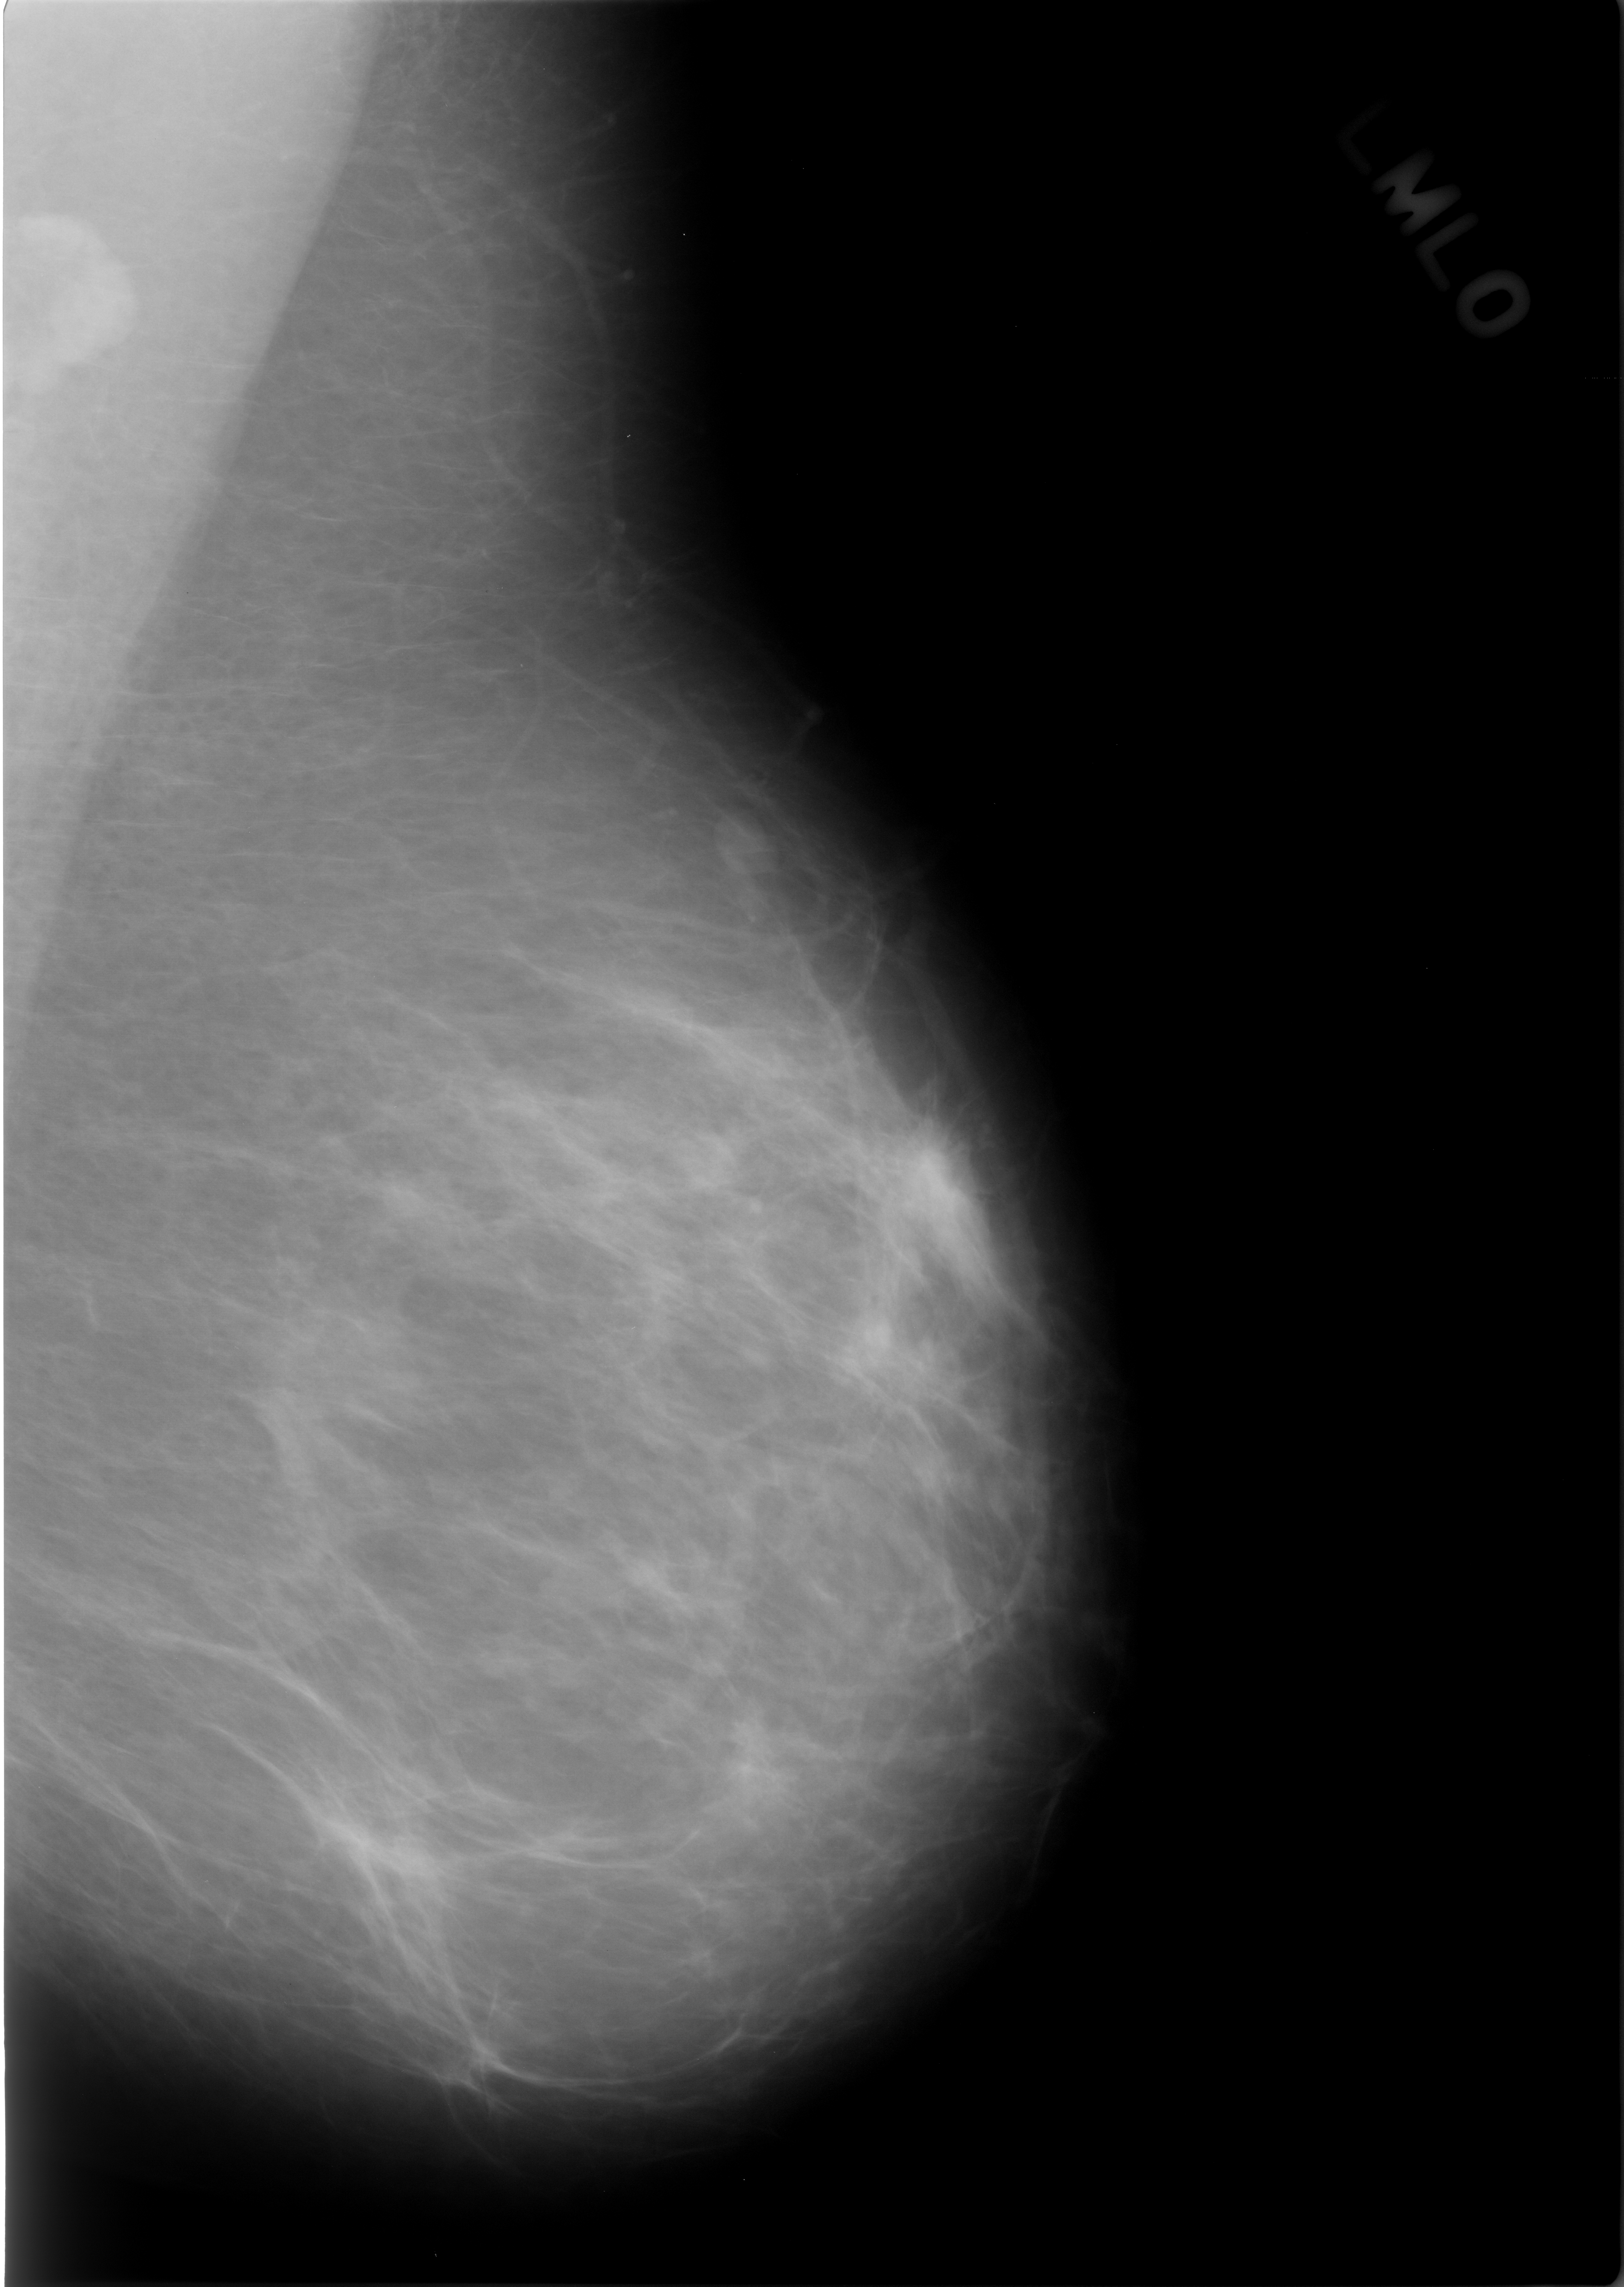
Digitized screen-film mammogram, left breast, mediolateral oblique (MLO) view, breast composition: almost entirely fatty (BI-RADS density category 1 of 4).
Mass, shape irregular, margins spiculated; BI-RADS assessment category 4; benign without callback (not worked up further).